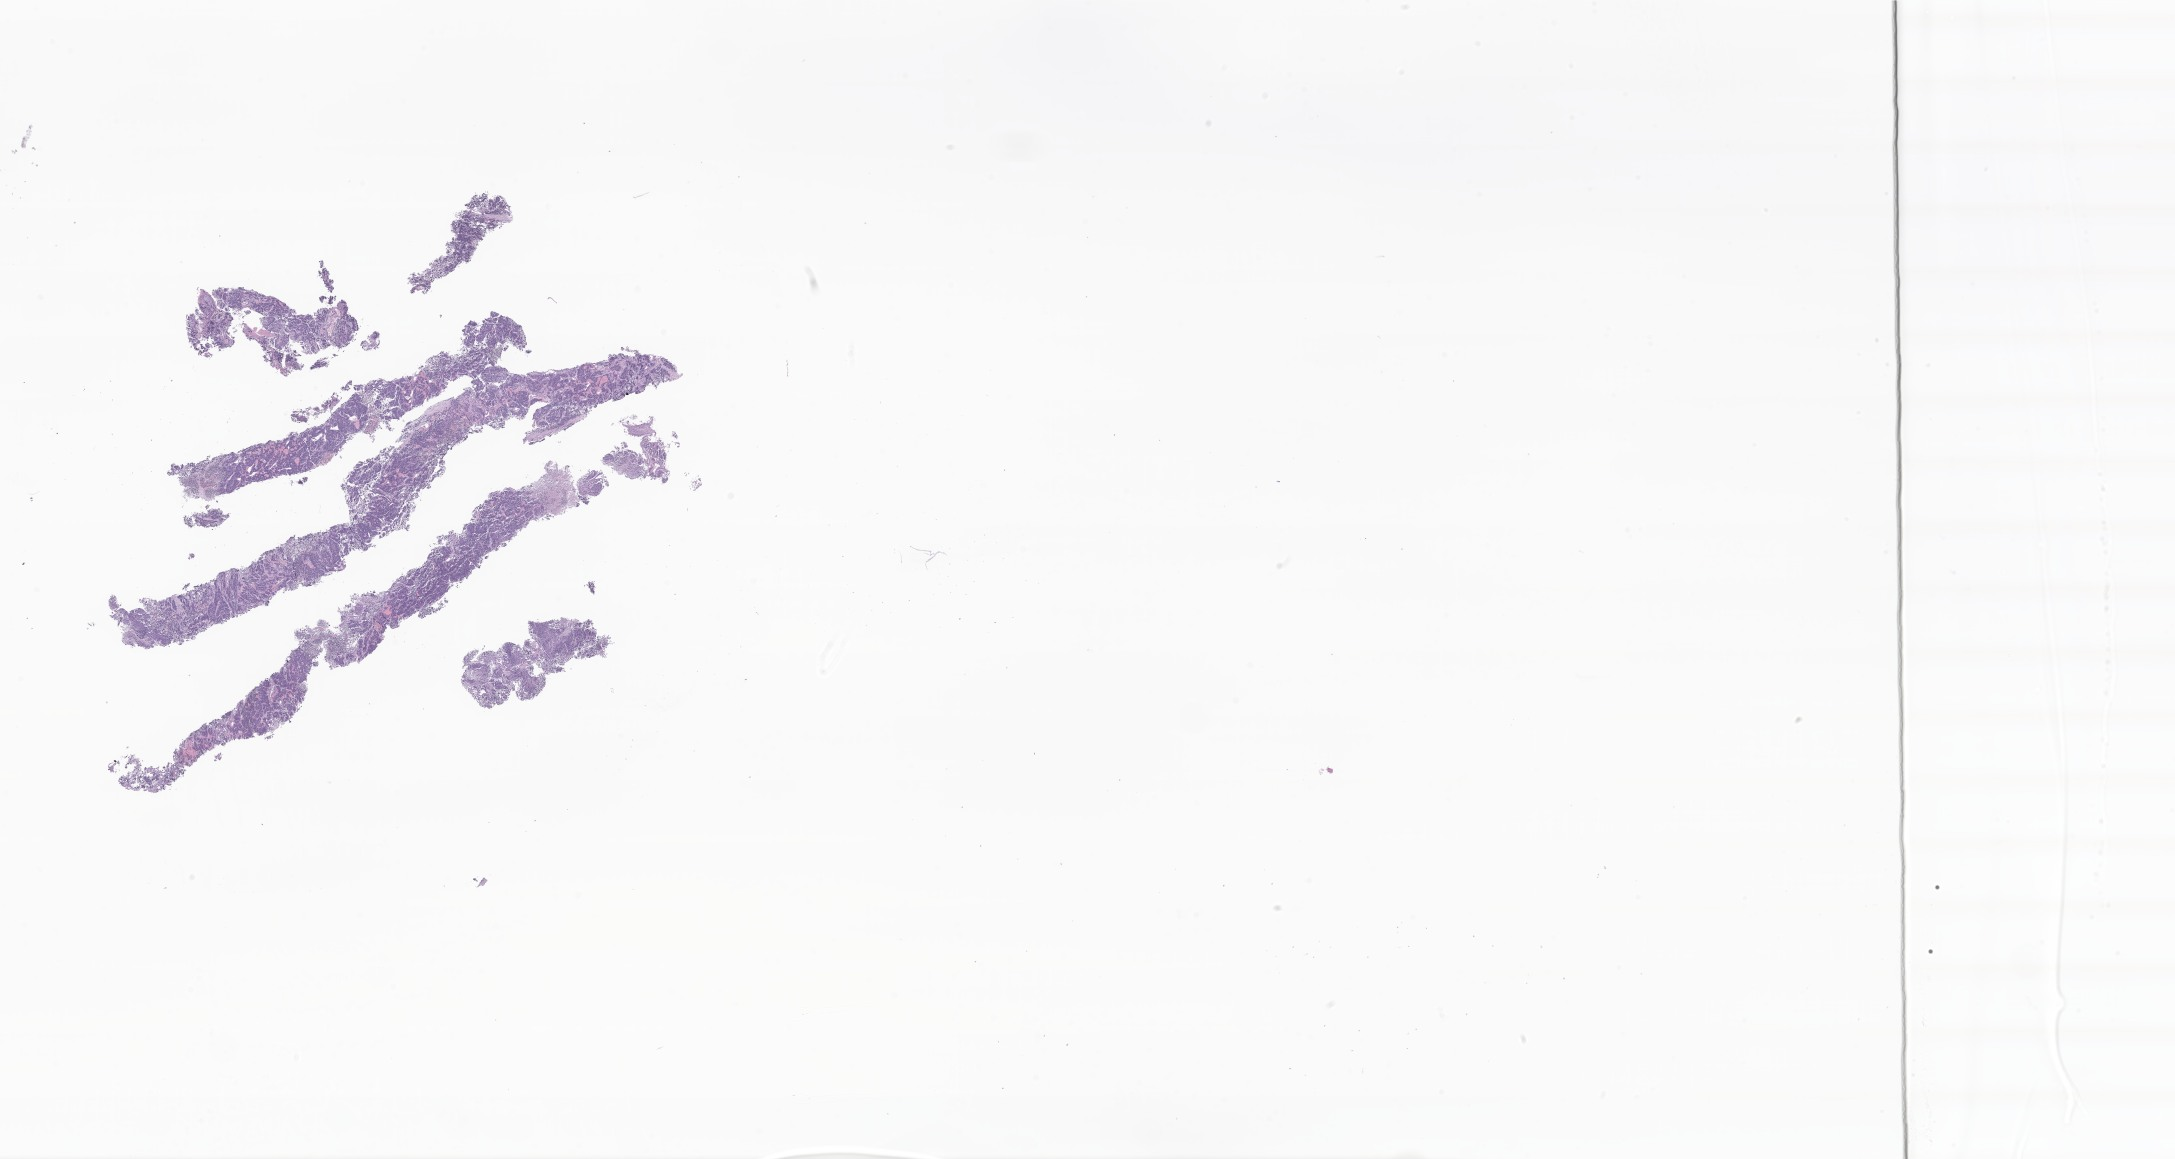
Digitized haematoxylin and eosin-stained section of tumor tissue from the head and neck, a low-resolution overview of the entire scanned area, about 36.7 x 19.6 mm. Formalin-fixed paraffin-embedded section. Patient: male, age 249 days.
• diagnosis (ICD-O-3 morphology term): Neuroblastoma, NOS